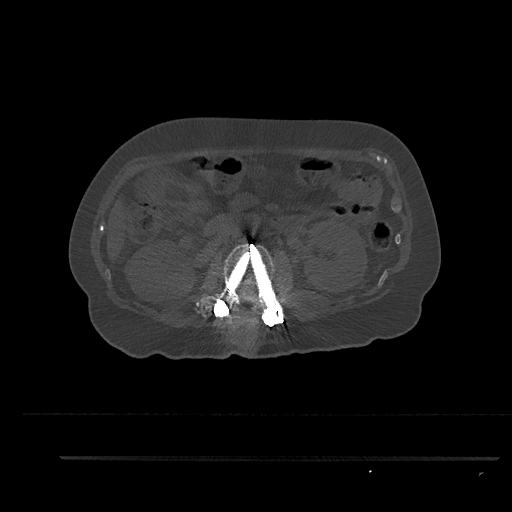
CT including the spine, one axial slice; slice 172 of 797 in the series (ordered by position); 120 kVp; bone window (W 1800 / L 400 HU); 0.5 mm slice thickness; 512 × 512 image matrix. Patient: female, 44 years. From the clinical record (not read from this slice): primary cancer: renal; vertebrae with lytic lesions (as recorded): L1.
Annotated regions visible in this slice (semi-automatic segmentation, software-assisted and operator-edited):
- L2 vertebra: box from (x=212, y=243) to (x=284, y=319) px